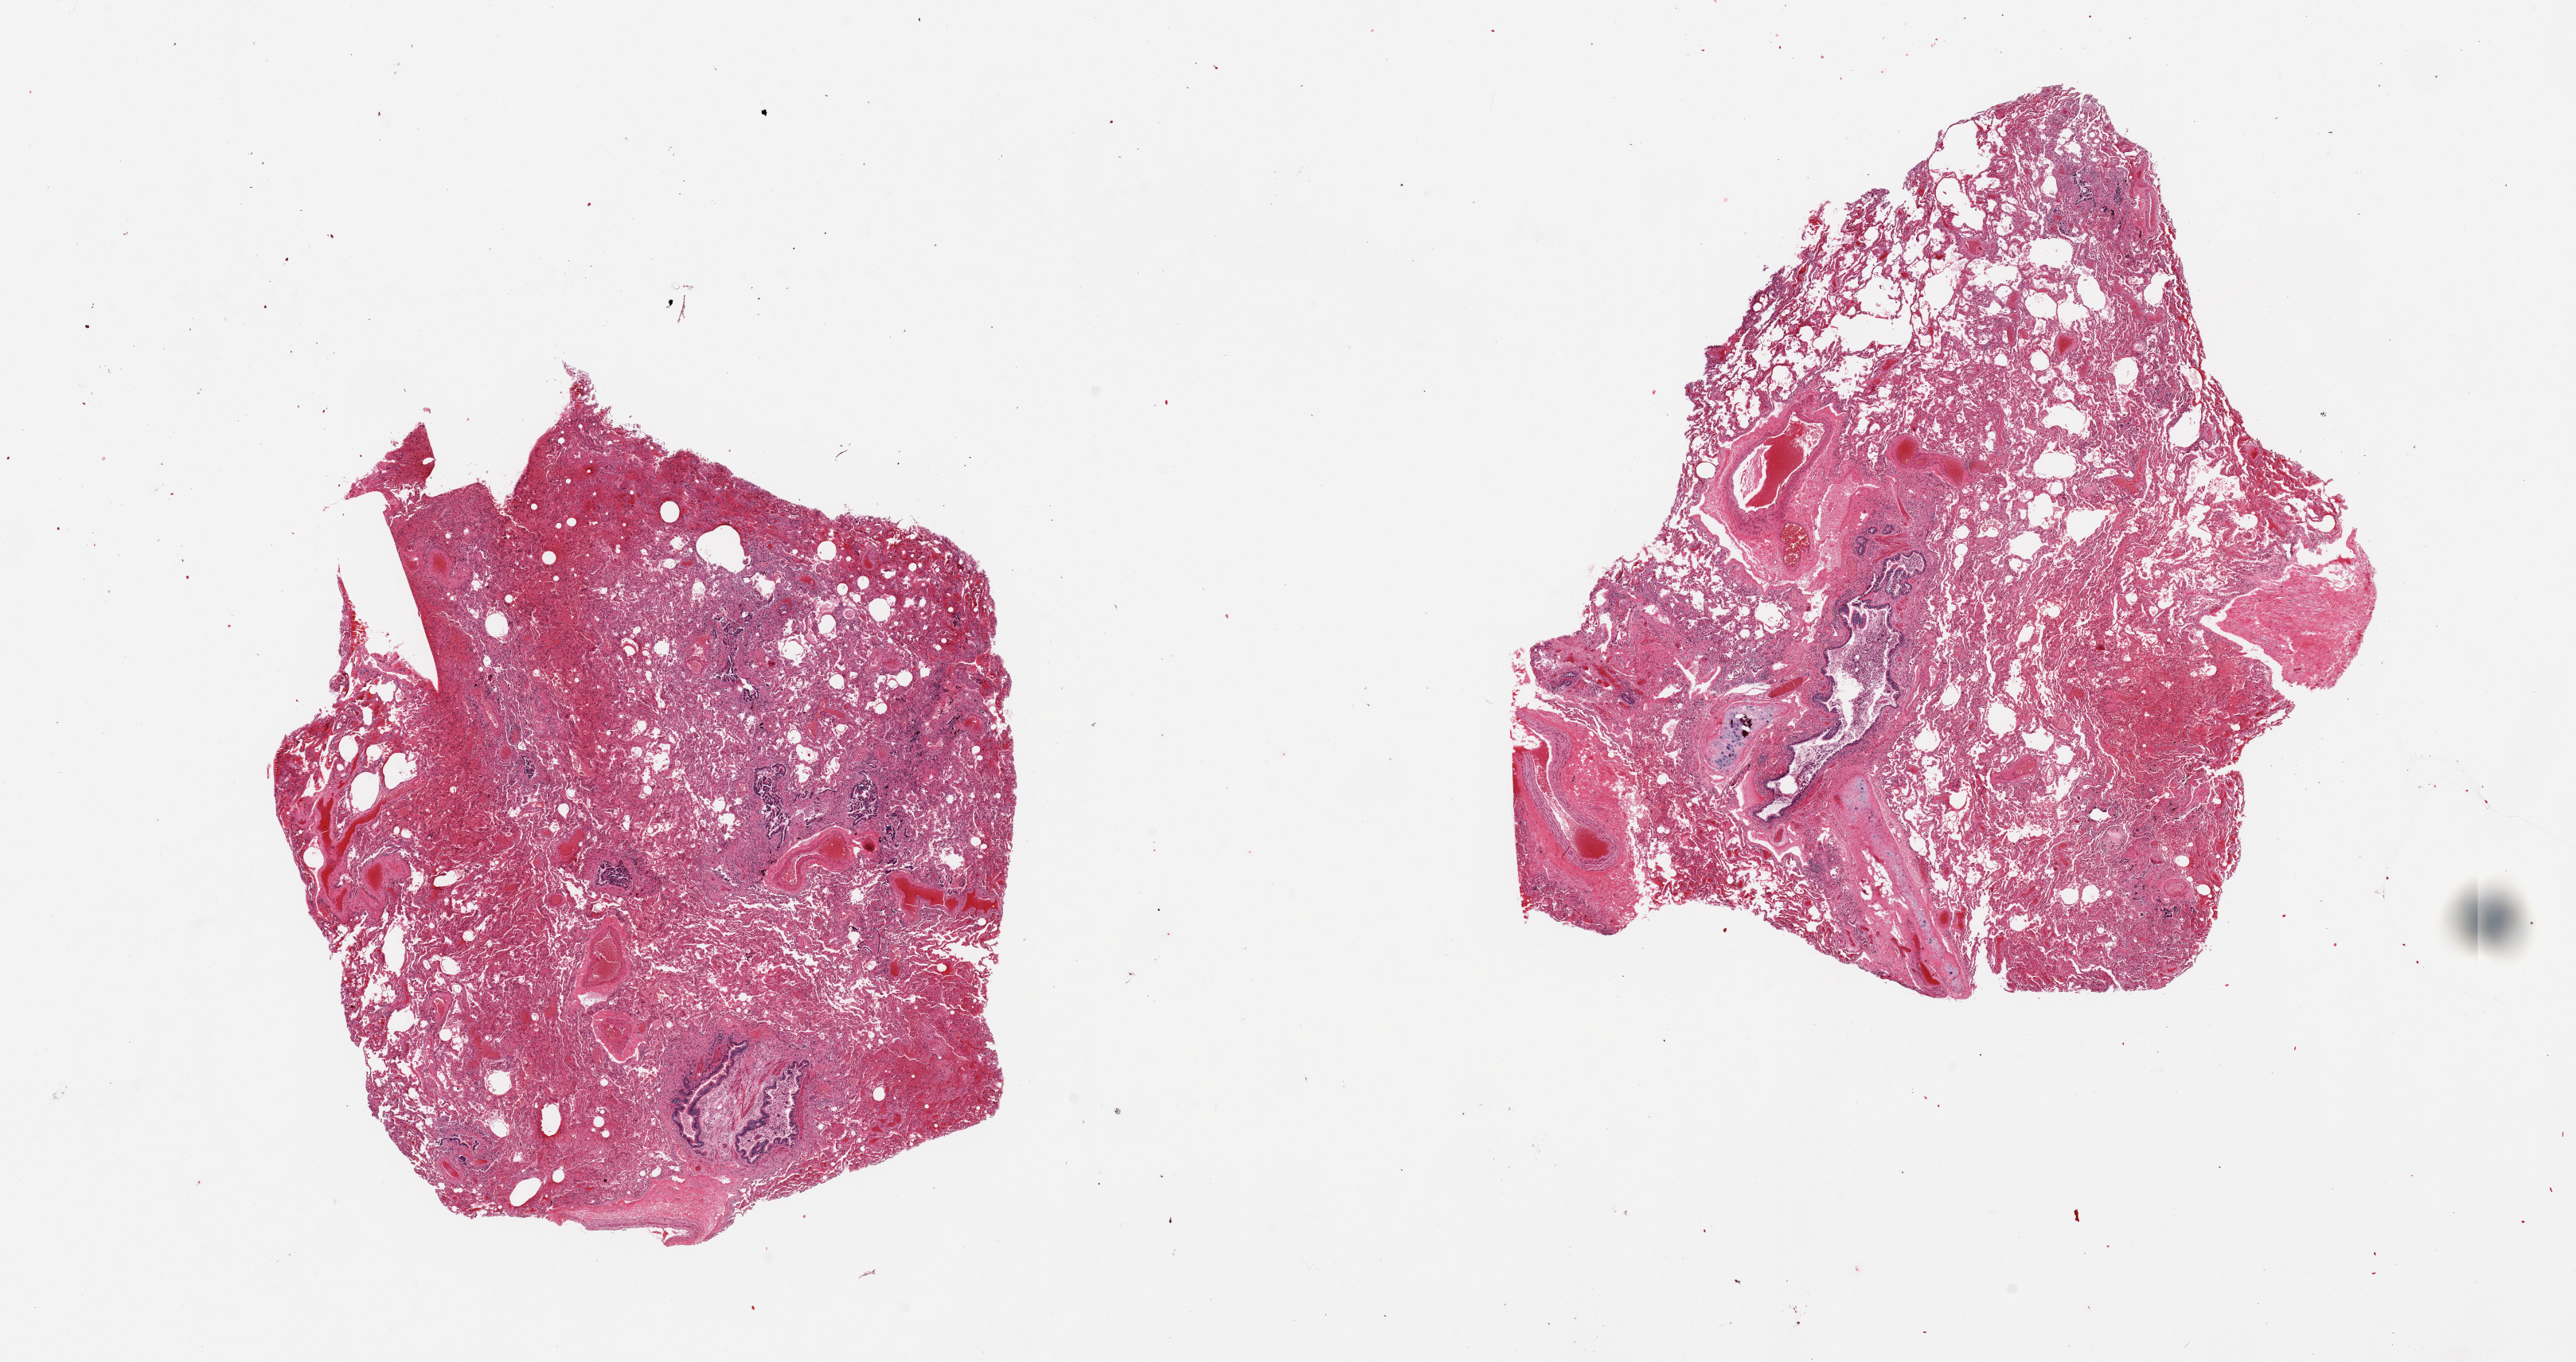
Hematoxylin and eosin (H&E) whole-slide image — shown as a low-resolution overview of the whole scanned area (about 25.6 x 13.5 mm). PAXgene-fixed, paraffin-embedded tissue. Target tissue: lung. Tissue donor sample. Donor: male.
* reviewer comment on this tissue sample: 2 pieces; debris in bronchi, congestion, patchy emphysema and focal alveolar hemorrhage